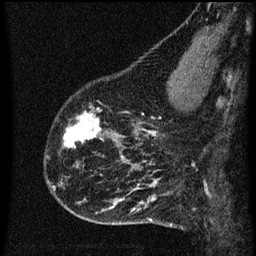
Breast MRI (dynamic contrast-enhanced), one sagittal slice. Slice 18 of 60 in the series (ordered by position). Dynamic contrast-enhanced series, image 2 of 3 at this slice position (ordered by acquisition). 1.5 T. TE 4.2 ms, TR 8 ms. 2 mm slice thickness. 256 × 256 image matrix. Female patient, age 43 years.
Structures marked on this image (semi-automatic segmentation, software-assisted and operator-edited):
- analysis volume of interest (the breast-tissue region the enhancement analysis was run in; not a lesion): box from (x=55, y=104) to (x=104, y=153) px
- tumour enhancement mask (voxels above the 70 % enhancement threshold inside the analysis volume of interest): (x=64, y=108)–(x=103, y=149)